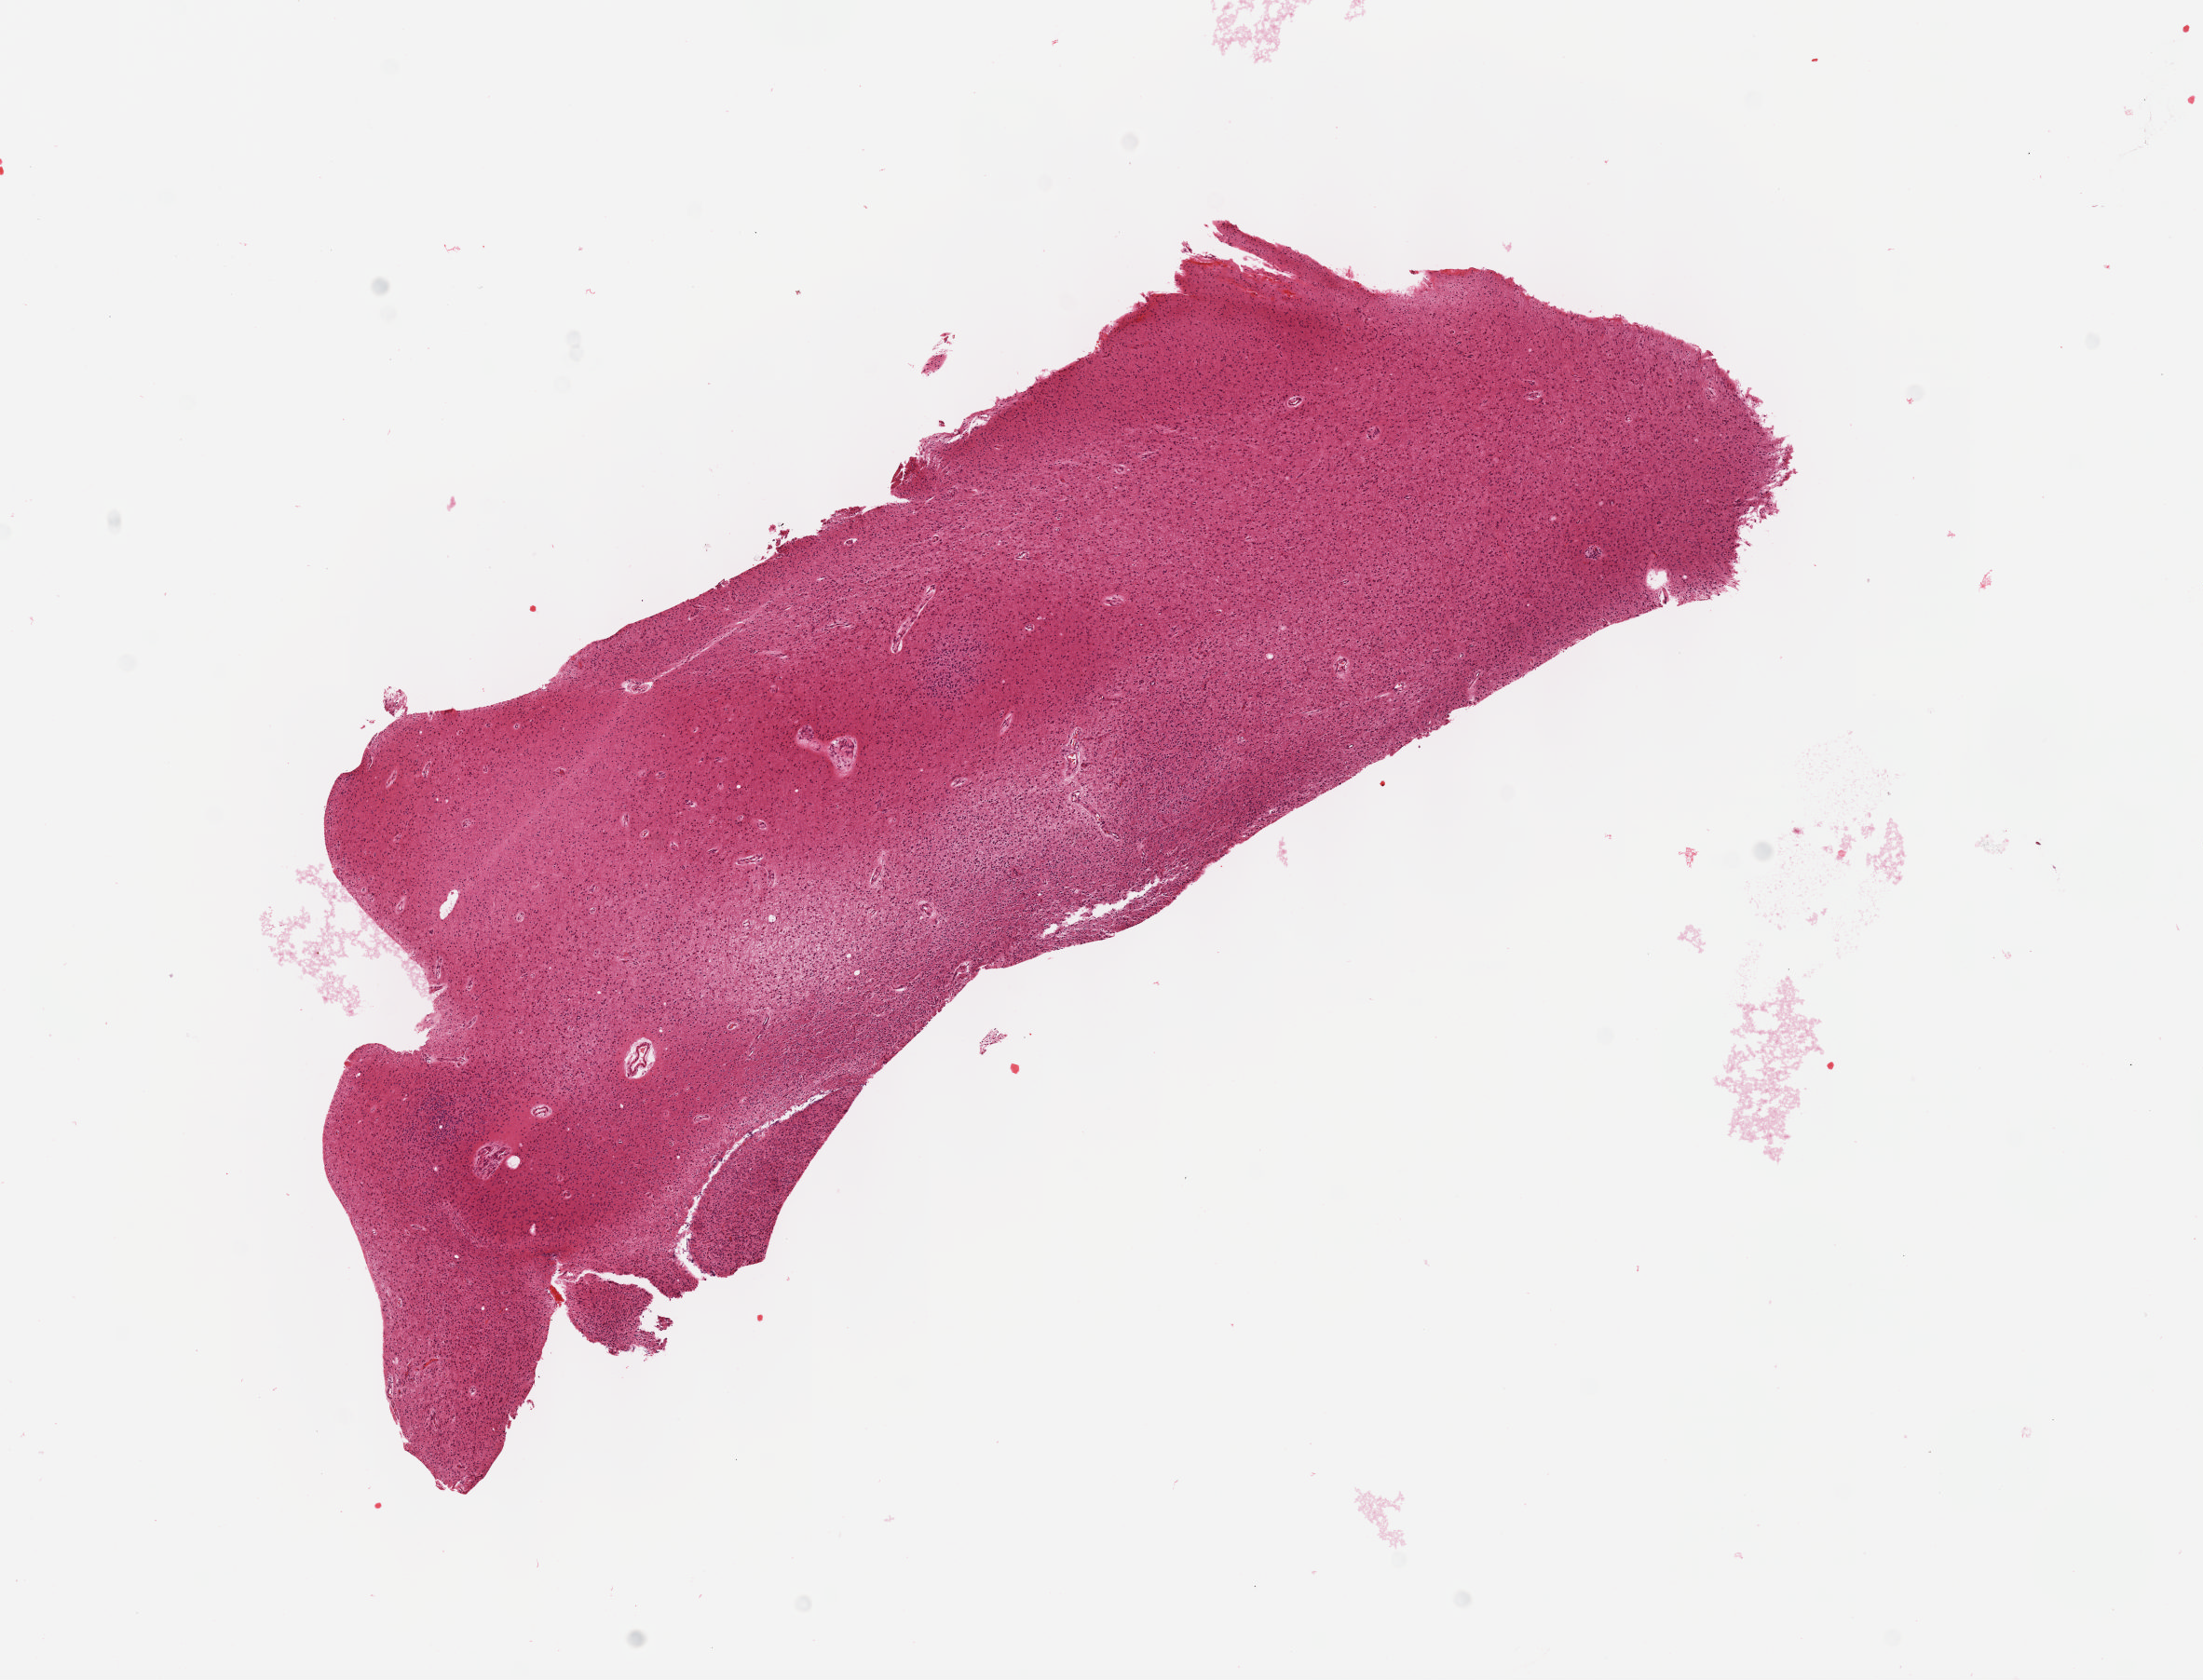
Digitized Hematoxylin and eosin (H&E) stained tissue section (whole slide) — shown as a low-resolution overview of the whole scanned area (about 9.6 x 7.3 mm, slide scanned at 40x). Formalin-fixed paraffin-embedded (FFPE) diagnostic section. Sample: primary tumour, brain. Male patient; age at initial diagnosis 45 years.
Diagnosis: Oligodendroglioma, NOS (cerebrum).